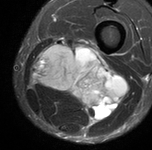
MRI of an extremity soft-tissue mass, one axial slice. Position 35 of 90 along the scan axis. STIR. MR volume resampled by the dataset authors to the PET/CT grid (not the native acquisition matrix). 152 × 150 image matrix, field of view 148 × 146 mm. Male patient. From the clinical record (not read from this slice): histological type: undifferentiated pleomorphic liposarcoma; grade: high; site of the primary tumour: left thigh.
Outlined on this slice (expert contour drawn on MRI and transferred to this co-registered scan by the dataset authors):
- gross tumour volume including surrounding oedema: bounding box [x1, y1, x2, y2] px = [32, 37, 124, 122]
- gross tumour volume (mass): [39, 50, 119, 113]